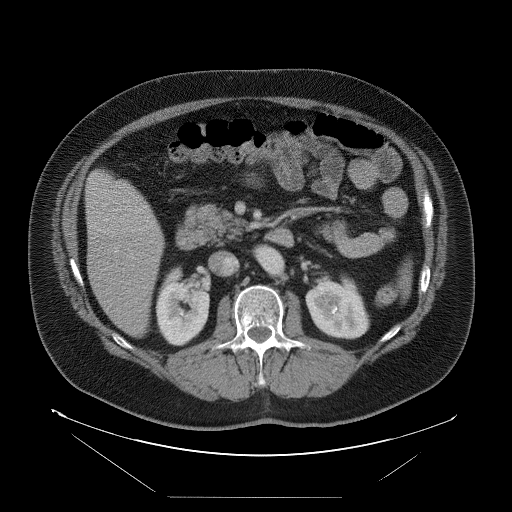
Contrast-enhanced abdominal CT, one axial slice; position 36 of 114 along the scan axis; 120 kVp; soft-tissue window (W 400 / L 40 HU); 512 × 512 image matrix, field of view 500 × 500 mm. Male patient, age 61 years. From the clinical record (not read from this slice): diagnosis: colorectal cancer liver metastases, imaged before liver resection; multiple liver metastases: no.
Structures marked on this image (outlined manually by an expert reader):
- liver: bounding box <86,171,165,337> (left, top, right, bottom; pixels)